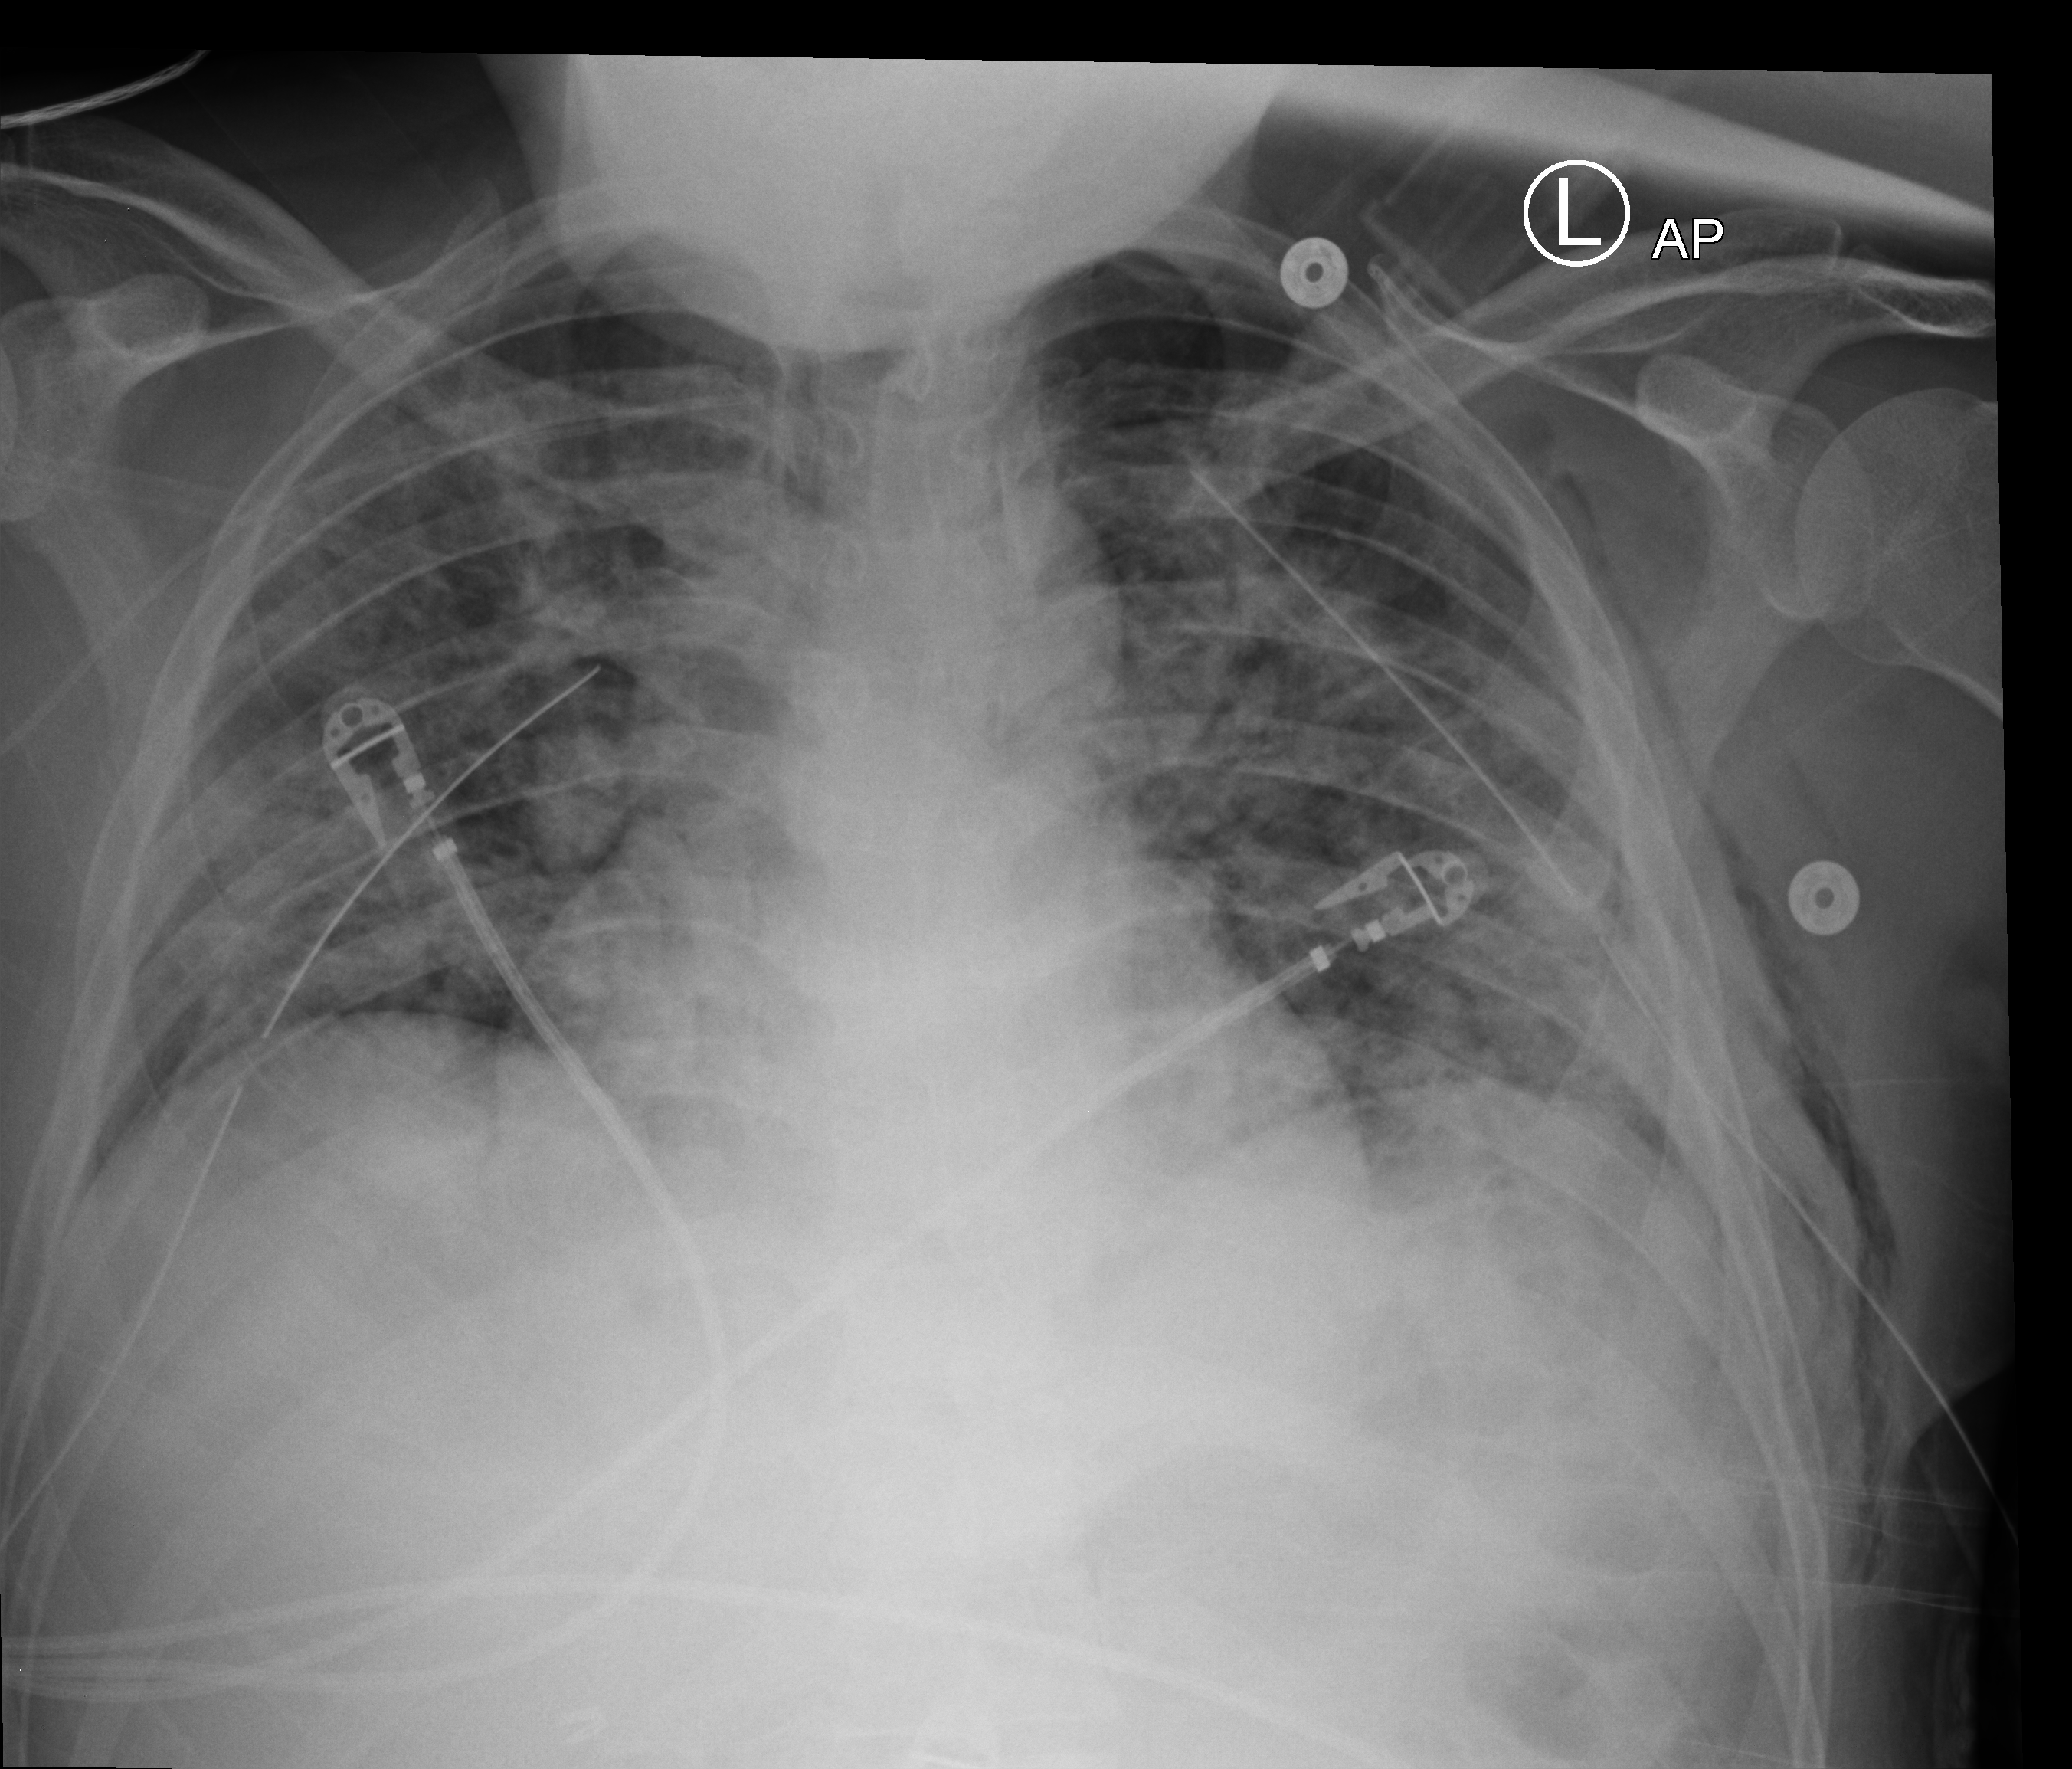
Chest X-ray (portable), anteroposterior (AP) projection. Male patient hospitalised with COVID-19, age 18–59 years.
Hospital-stay facts (about this admission, not read from this image; timing relative to this image not recorded):
- other chronic lung disease (admission record): no
- admitted to intensive care during this hospital stay: yes